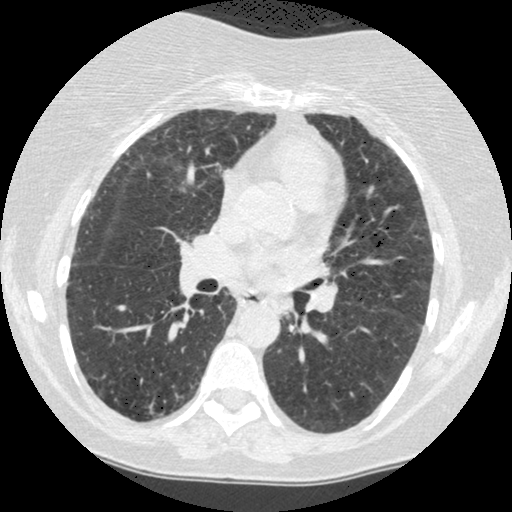
Low-dose screening chest CT, axial slice, baseline annual screen, lung window (W 1500 / L -600 HU), 1.25 mm slice thickness, standard (soft-tissue) reconstruction kernel (STANDARD). Female participant, aged 60 years at enrolment.
Expert reader's lesion annotation, bounding box (x1, y1, x2, y2) in pixels: (266, 290, 308, 331). The screening reader recorded 2 non-calcified nodules or masses ≥4 mm on this exam (right lower lobe, left lower lobe); which of them this box marks is not recorded. Later outcome: lung cancer diagnosed 794 days after this screen (after the third annual screen) — small cell carcinoma, NOS, left lower lobe, undifferentiated (G4), stage IV (AJCC 6th edition), 69 mm at pathology.